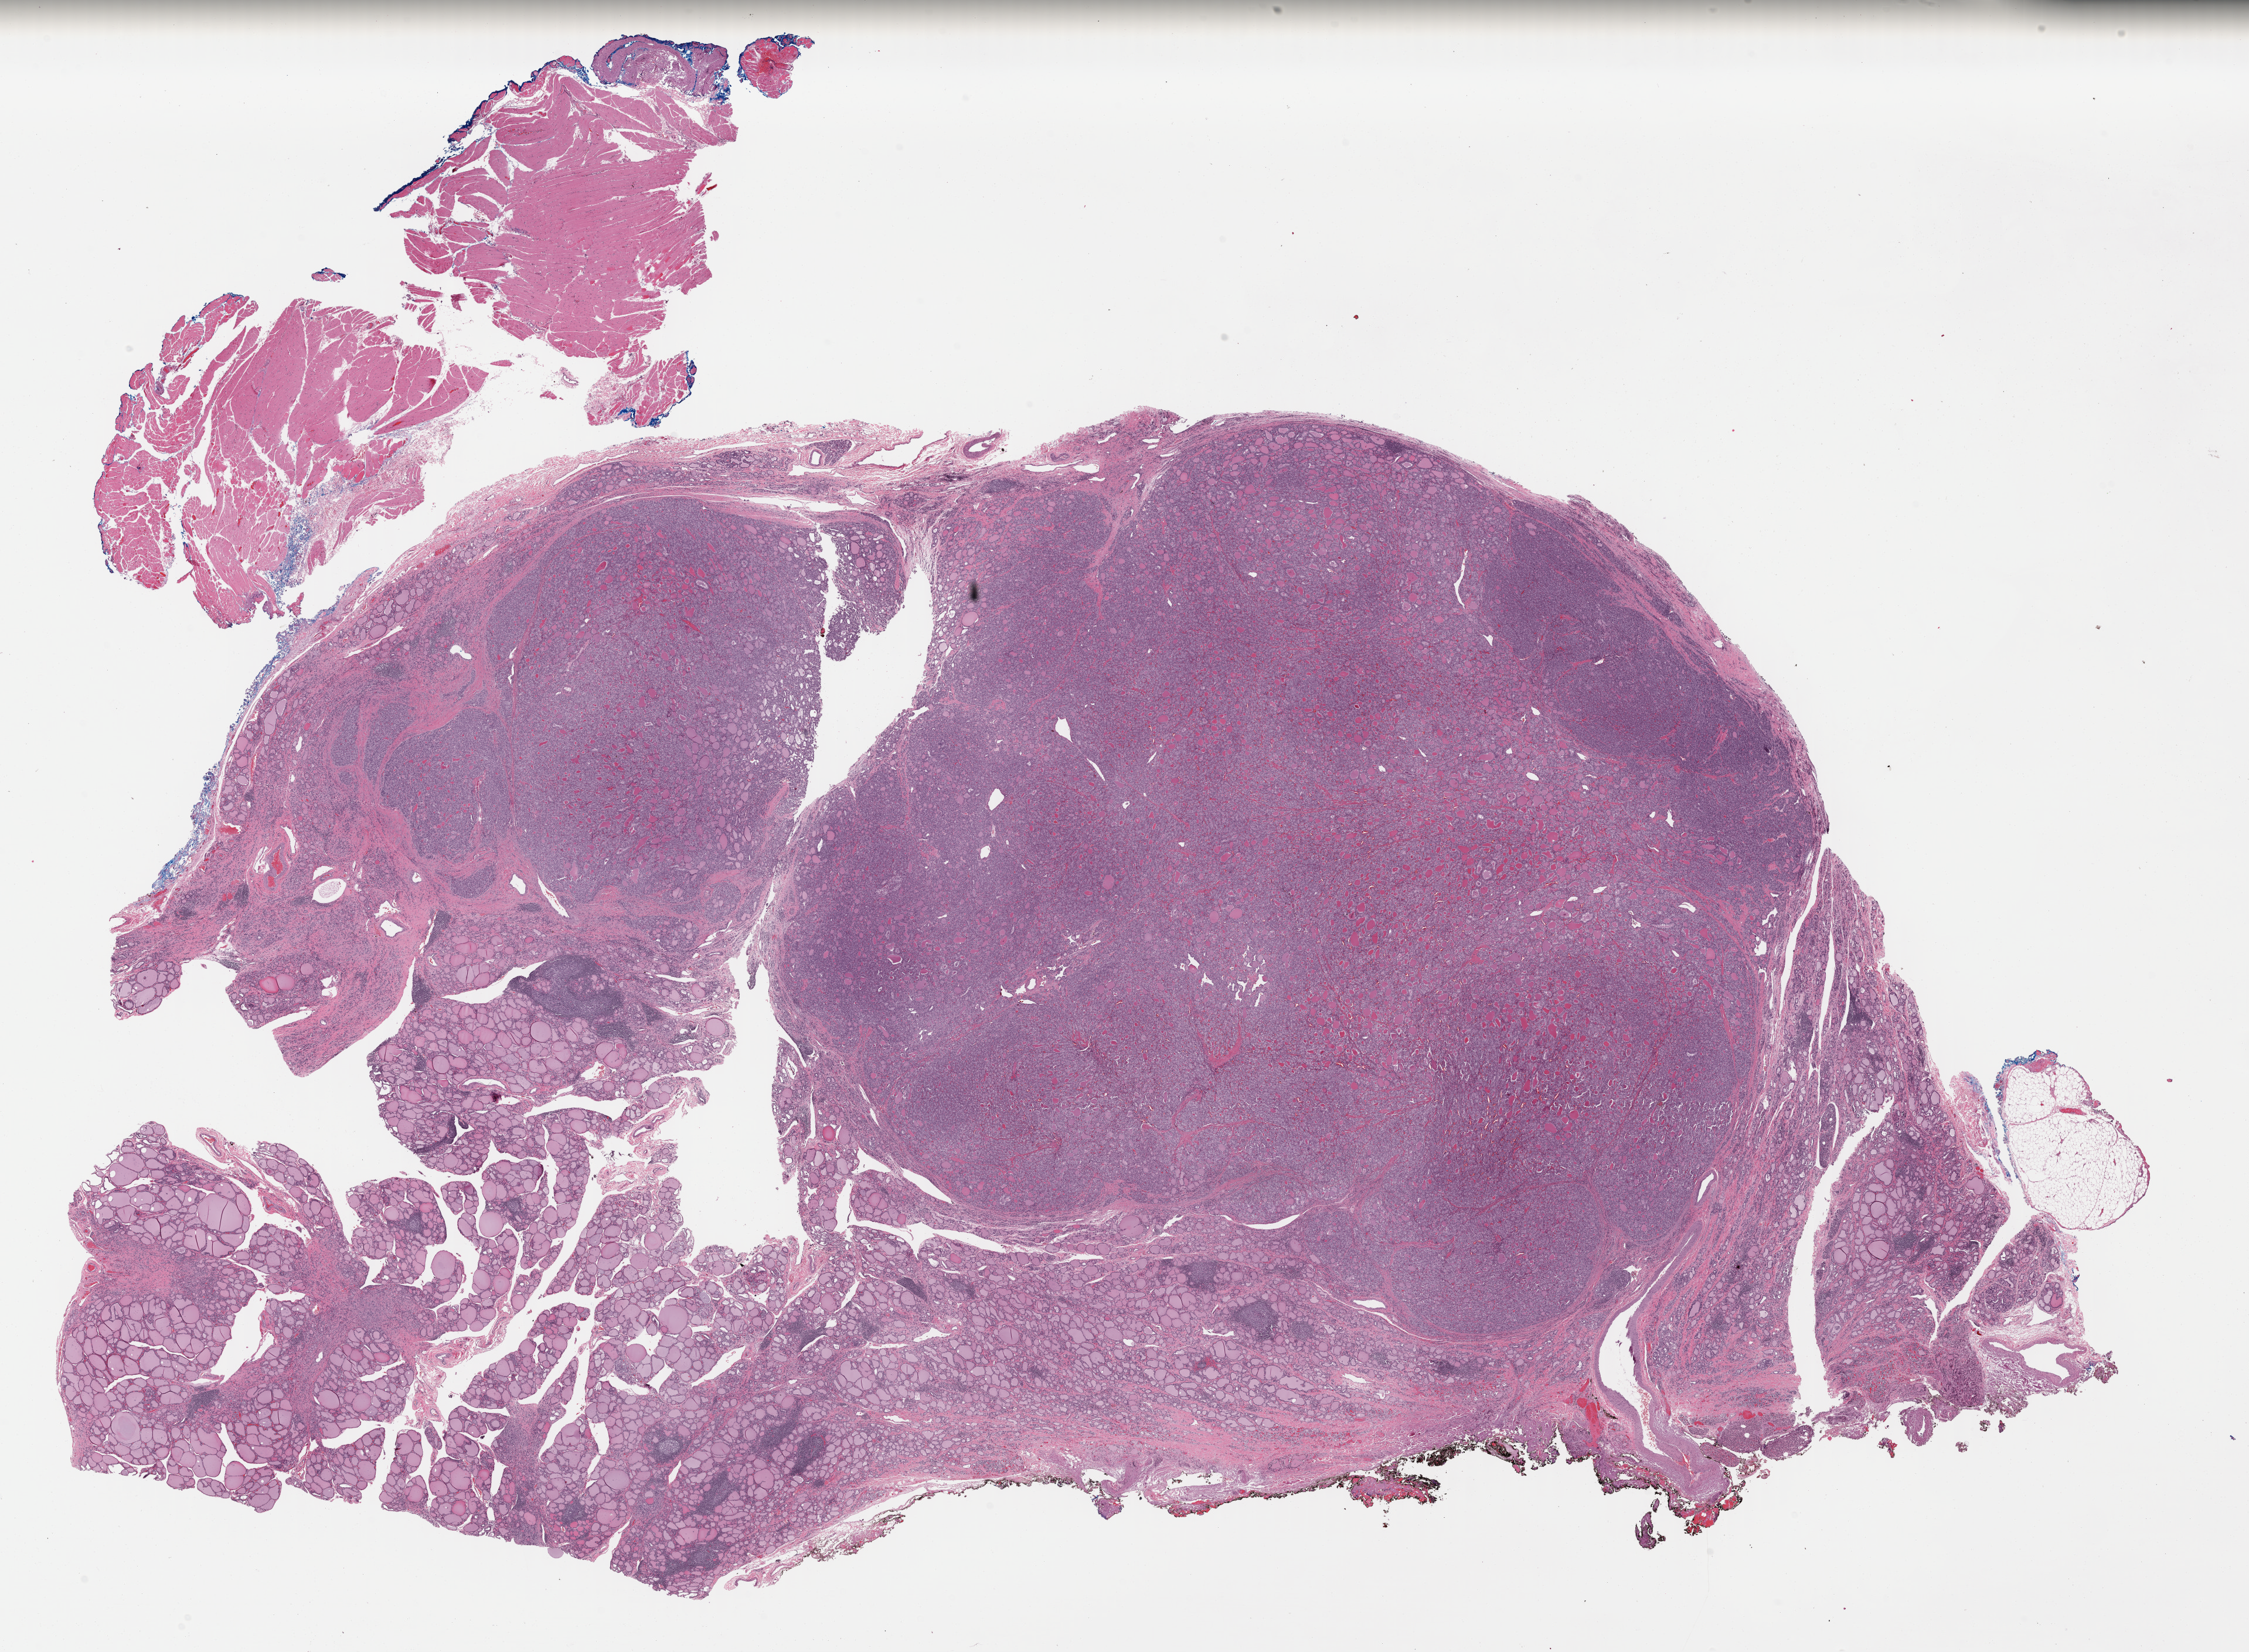
Hematoxylin and eosin (H&E) stained whole-slide image — shown as a low-resolution overview of the whole scanned area (about 30.2 x 22.2 mm, from a 40x scan). FFPE section. Thyroid, primary tumour sample. Patient: female, age at initial diagnosis 36 years.
• AJCC pathologic stage: II (7th edition)
• TNM: T3 N1b M1
• lymph nodes positive (case pathology): 11 of 23 examined
• histologic diagnosis: Papillary carcinoma, follicular variant (thyroid gland)